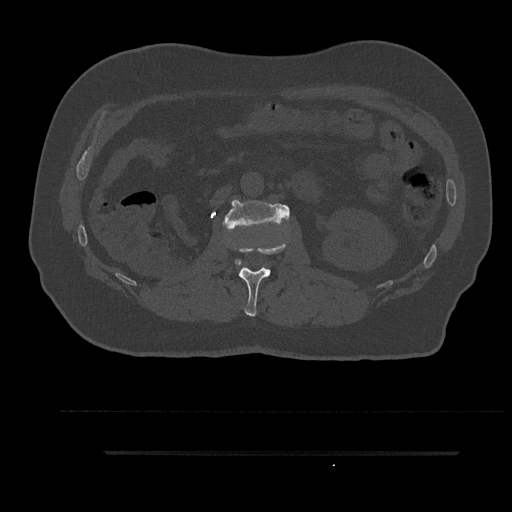
CT including the spine, one axial slice; 120 kVp; bone window (W 1800 / L 400 HU); 0.5 mm slice thickness; 512 × 512 image matrix, field of view 432 × 432 mm. Patient: male, 63 years. Case-level facts recorded for this patient, not image findings: primary cancer: renal; vertebrae with lytic lesions (as recorded): T8.
Structures marked on this image (semi-automatic segmentation, software-assisted and operator-edited):
- L1 vertebra: bounding box <238,243,286,317> (left, top, right, bottom; pixels)
- L2 vertebra: <223,199,290,265>